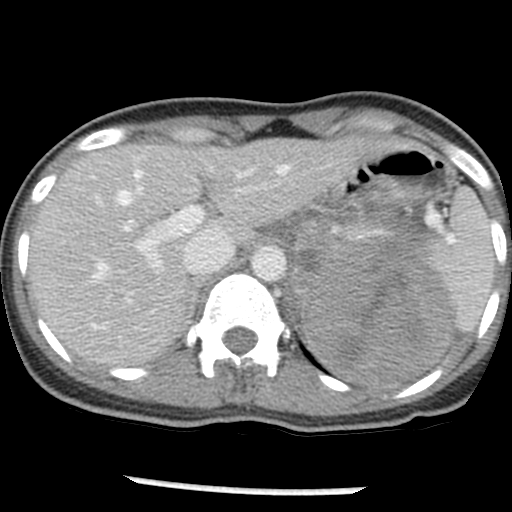
Contrast-enhanced abdominal CT, one axial slice. Position 35 of 54 along the scan axis. Intravenous contrast given. Soft-tissue window (W 400 / L 40 HU). 5 mm slice thickness. 512 × 512 image matrix, field of view 240 × 240 mm. Female patient, age 33 years. From the clinical record (not read from this slice): diagnosis: adrenocortical carcinoma; tumour side: left adrenal; tumour size at pathology: 11 cm; Ki-67 index: 20 %; stage (as recorded): 2.
Outlined on this slice (semi-automatic segmentation, software-assisted and operator-edited):
- mass: bounding box [x1, y1, x2, y2] px = [289, 206, 457, 388]